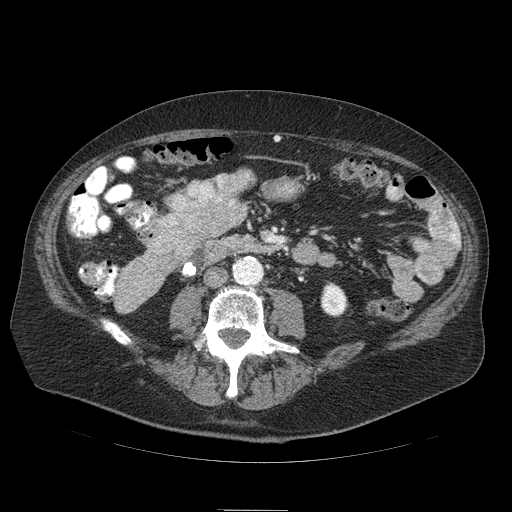
Contrast-enhanced abdominal CT (liver protocol), one axial slice. Position 12 of 103 along the scan axis. 120 kVp. Soft-tissue window (W 400 / L 40 HU). 2.5 mm slice thickness. 512 × 512 image matrix, field of view 440 × 440 mm. Case-level facts recorded for this patient, not image findings: diagnosis: hepatocellular carcinoma (patient treated with transarterial chemoembolisation; whether this scan precedes or follows treatment is not stated here); TNM stage (as recorded): Stage-IIIA; Child-Pugh class: B; tumour differentiation: well differentiated.
Structures marked on this image (semi-automatically segmented with operator editing):
- mass: bounding box <150,200,246,265> (left, top, right, bottom; pixels)